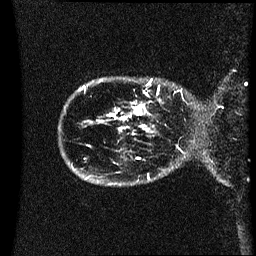
Breast MRI (dynamic contrast-enhanced), one sagittal slice; position 4 of 60 along the scan axis; dynamic contrast-enhanced series, image 2 of 3 at this slice position (ordered by acquisition); 1.5 T; TE 4.2 ms, TR 8.4 ms; 256 × 256 image matrix. Female patient, age 41 years. Case-level facts recorded for this patient, not image findings: setting: breast cancer imaged before/during neoadjuvant chemotherapy; receptor status: HER2-positive.
Annotated regions visible in this slice (semi-automatically segmented with operator editing):
- analysis volume of interest (the breast-tissue region the enhancement analysis was run in; not a lesion): bounding box <122,80,187,121> (left, top, right, bottom; pixels)
- tumour enhancement mask (voxels above the 70 % enhancement threshold inside the analysis volume of interest): <122,104,146,121>